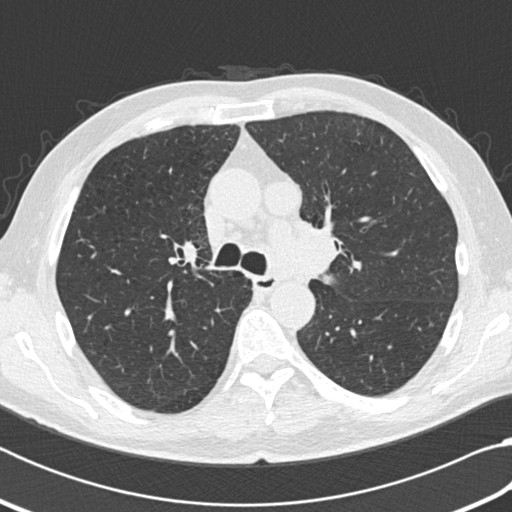
Chest CT (low-dose screening protocol), one axial image. Third screening round (two years after baseline). Lung window (W 1500 / L -600 HU). 2 mm slice thickness. Standard (soft-tissue) reconstruction kernel (B30f). Male, age 64 years at enrolment.
Expert-annotated lung lesion, box from (x=252, y=175) to (x=299, y=218) px. No non-calcified nodule or mass ≥4 mm was recorded by the screening reader at this exam. Later outcome: lung cancer diagnosed 163 days after this screen — small cell carcinoma, NOS, mediastinum, stage IV (AJCC 6th edition).